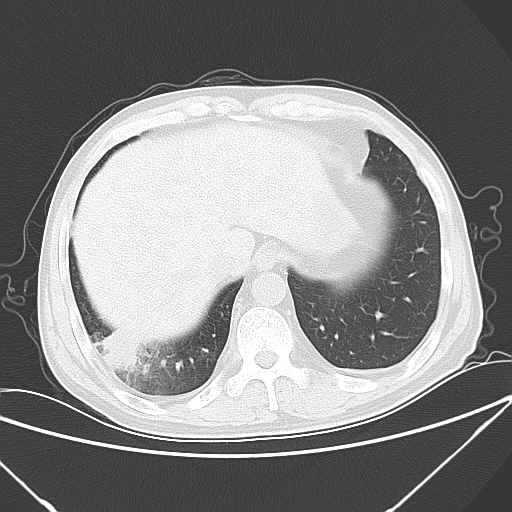
Chest CT, one axial slice. Position 15 of 57 along the scan axis. 120 kVp. Lung window (W 1500 / L -600 HU). 512 × 512 image matrix, field of view 364 × 364 mm. Male patient, age 54 years. From the clinical record (not read from this slice): clinical TNM (as recorded): T2 N1 M0; histopathological grade: G3.
Structures marked on this image (rectangle marked by the reading radiologist):
- lung tumour (recorded histology: adenocarcinoma): box from (x=97, y=327) to (x=141, y=369) px